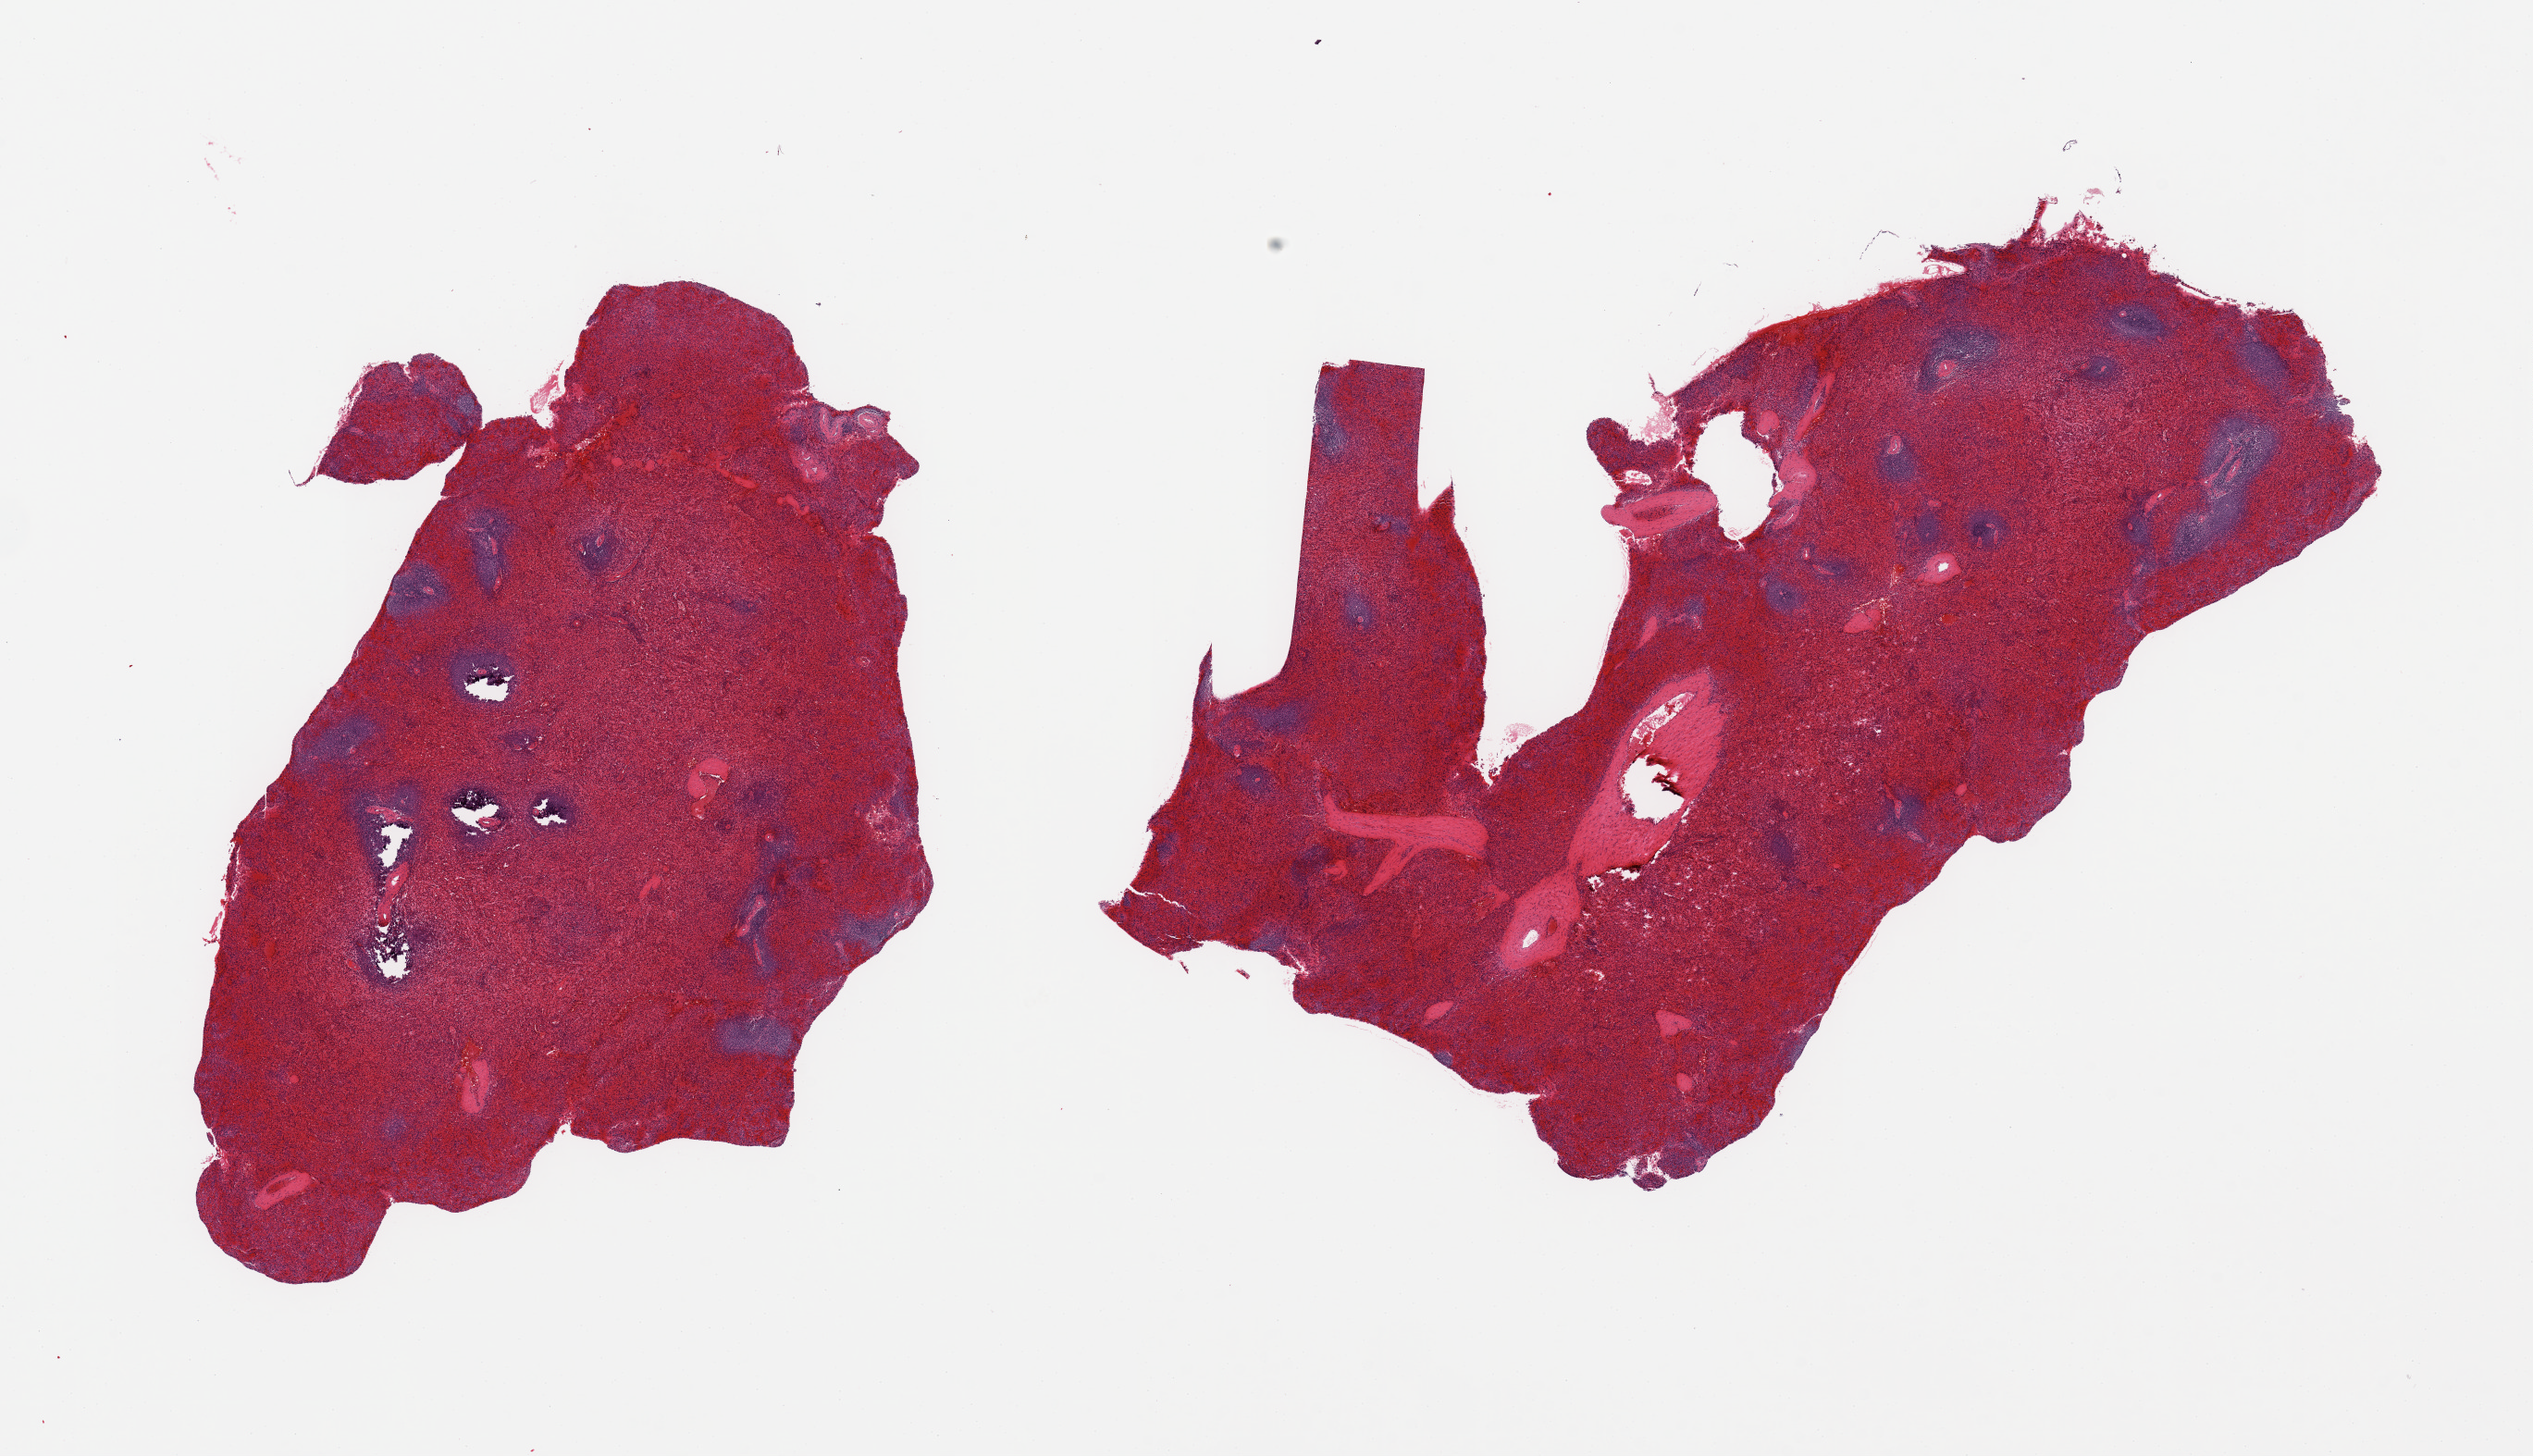
Hematoxylin and eosin (H&E) whole-slide image, whole scanned area (about 21.7 x 12.5 mm, acquisition: 20x scan) shown as a low-resolution overview, PAXgene-fixed paraffin-embedded (PFPE) section, target tissue: spleen, tissue donor sample. Donor: male.
- review note (as recorded): 2 pieces, no abnormalities